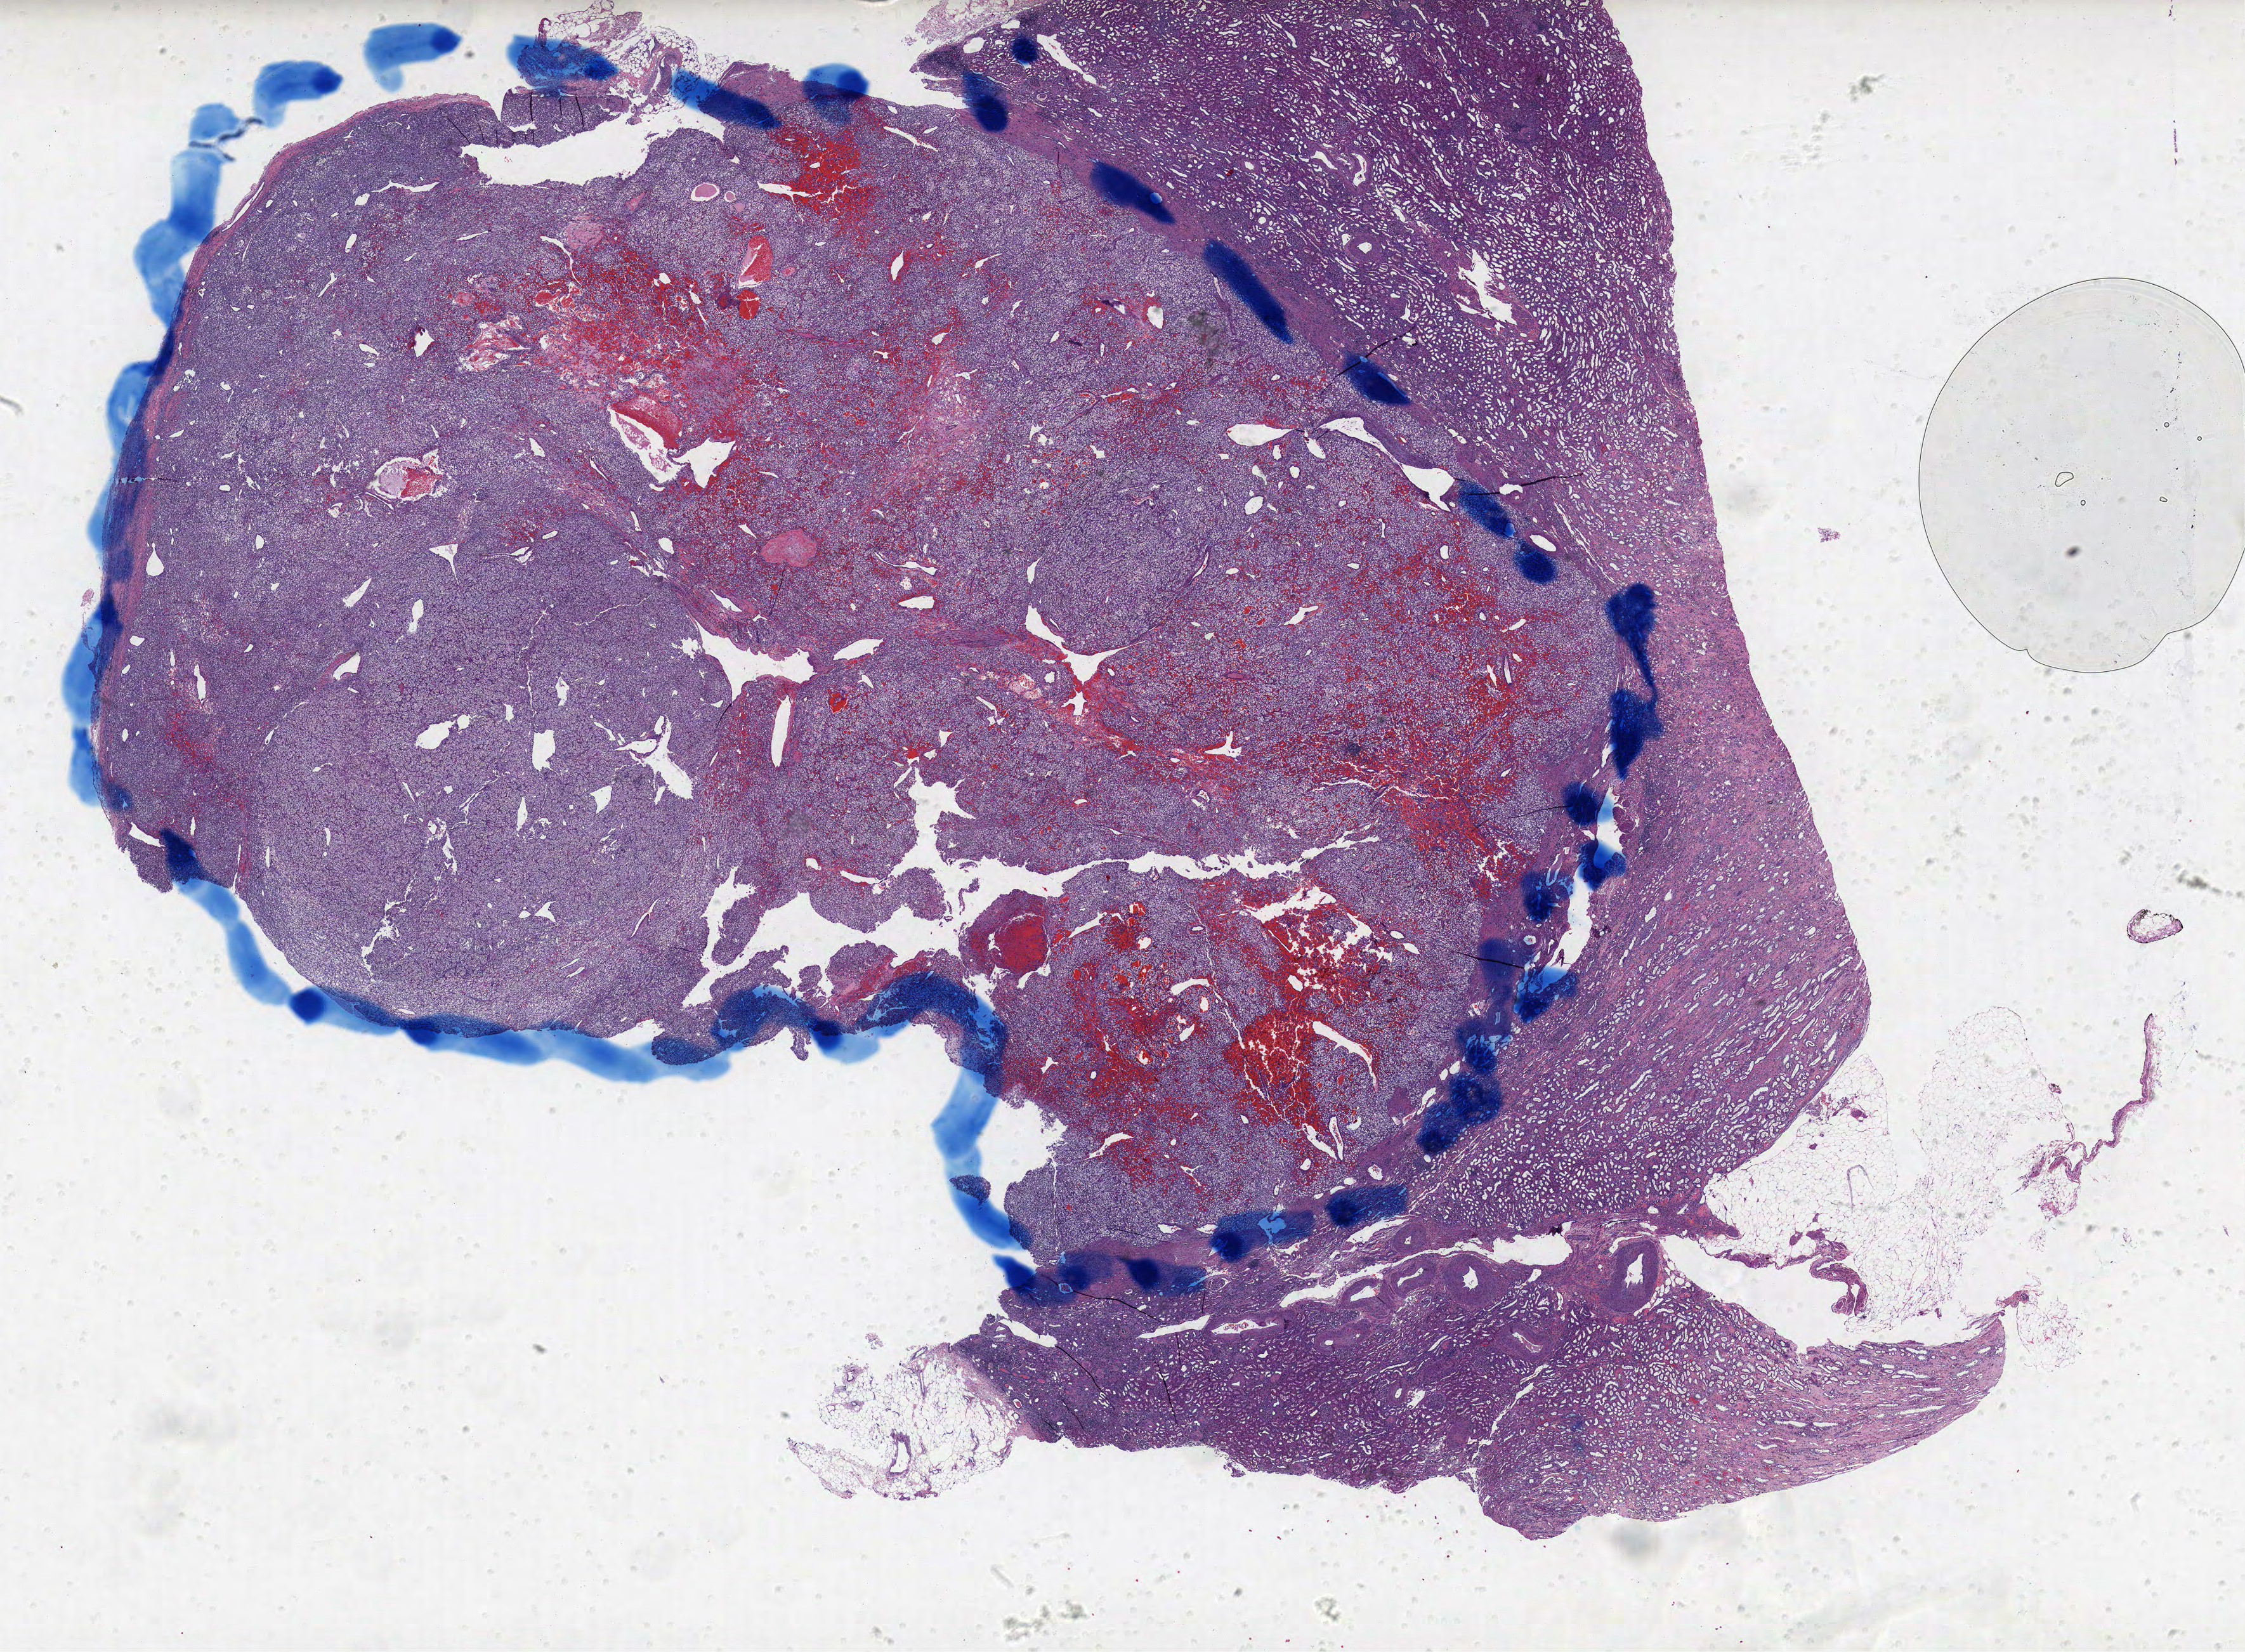
Whole-slide histology image, H&E-stained — shown as a low-resolution overview of the whole scanned area (about 28.3 x 20.8 mm, from a 40x scan). FFPE section. Sample: primary tumour, kidney. Female patient; age at initial diagnosis 79 years. Histologic grade: G2 (moderately differentiated).
Diagnosis: Clear cell adenocarcinoma, NOS. AJCC pathologic stage: I. TNM: T1a NX M0.